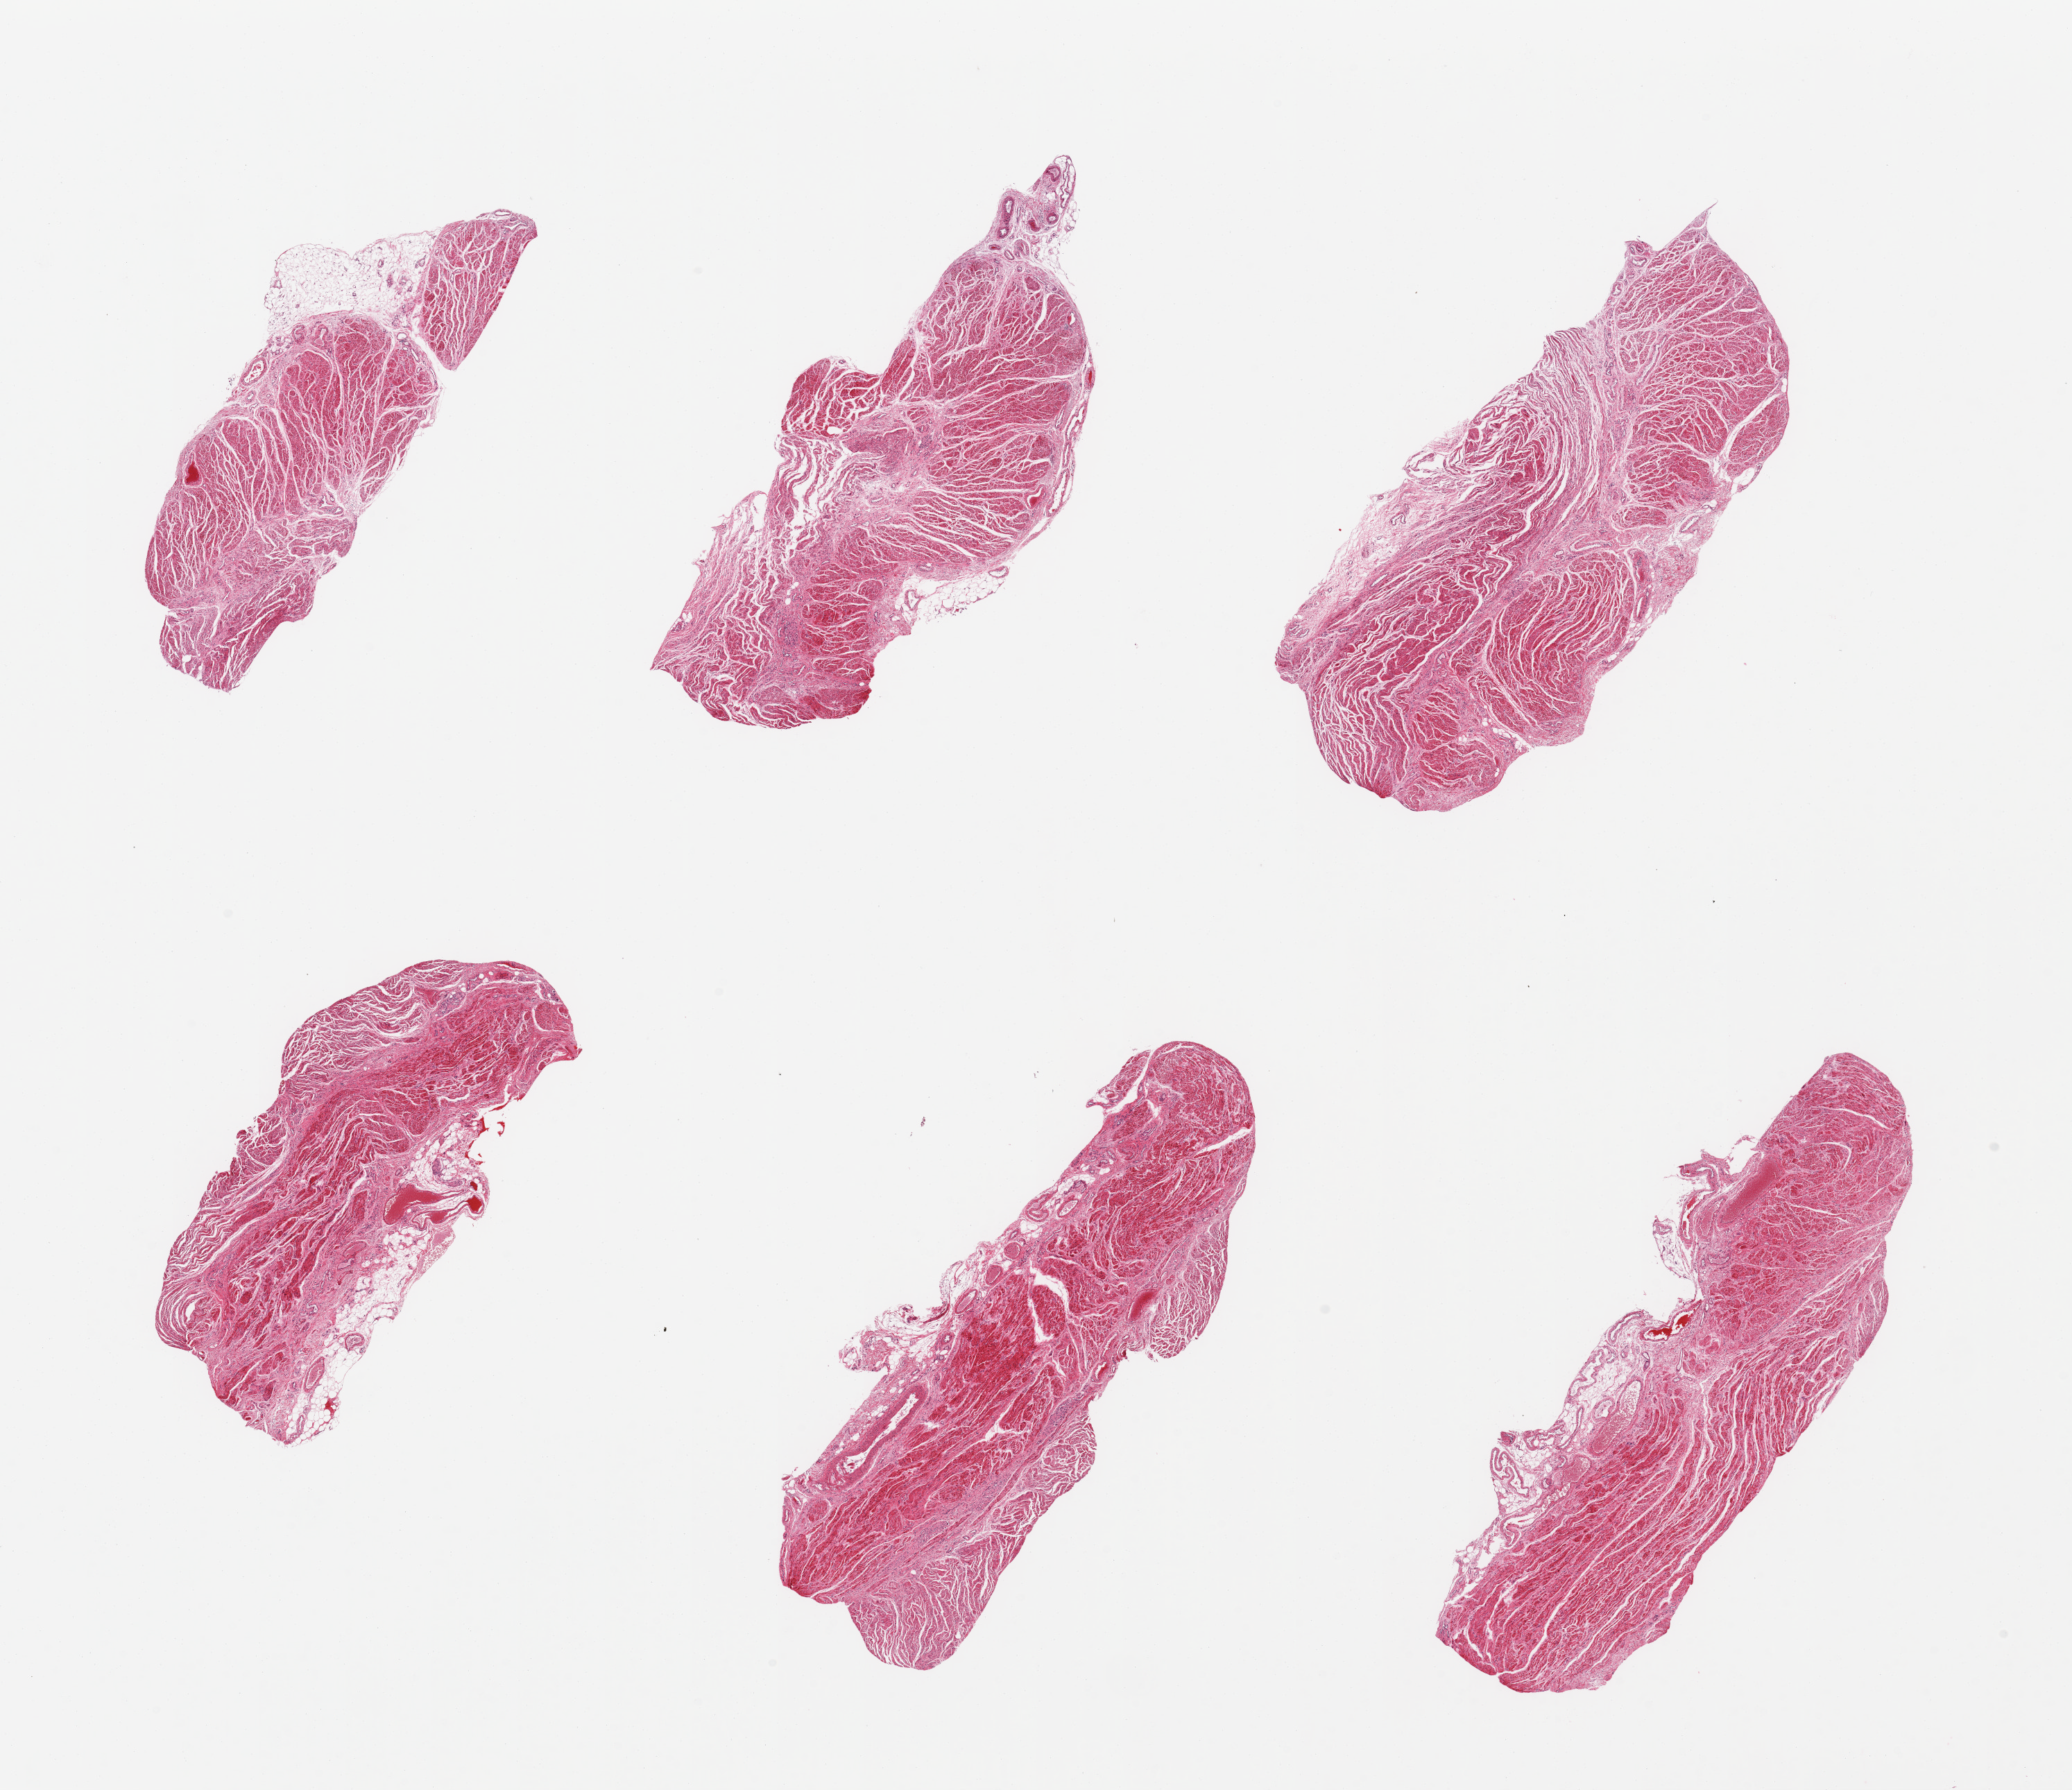
H&E whole-slide image, brightfield, whole scanned area (about 23.6 x 20.4 mm, acquisition: 20x scan) shown as a low-resolution overview, PAXgene-fixed, paraffin-embedded tissue, section of gastroesophageal junction (target tissue), donor tissue sample. Donor: female.
* reviewer comment on this tissue sample: 6 pieces; target muscularis, few pieces include small portion of fat (up to 10%)